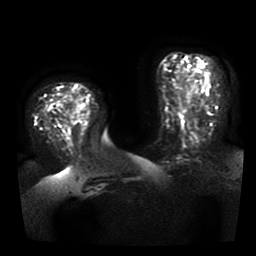
Breast MRI, one axial slice. Position 16 of 41 along the scan axis. Diffusion-weighted series; image 2 of 4 stored at this slice position (different b-values; order by instance number). 1.5 T. 5 mm slice thickness. 256 × 256 image matrix, field of view 330 × 330 mm. Female patient.
Structures marked on this image (outlined manually by an expert reader):
- tumour on diffusion-weighted imaging: bounding box (x1, y1, x2, y2) in pixels: (74, 101, 86, 112)